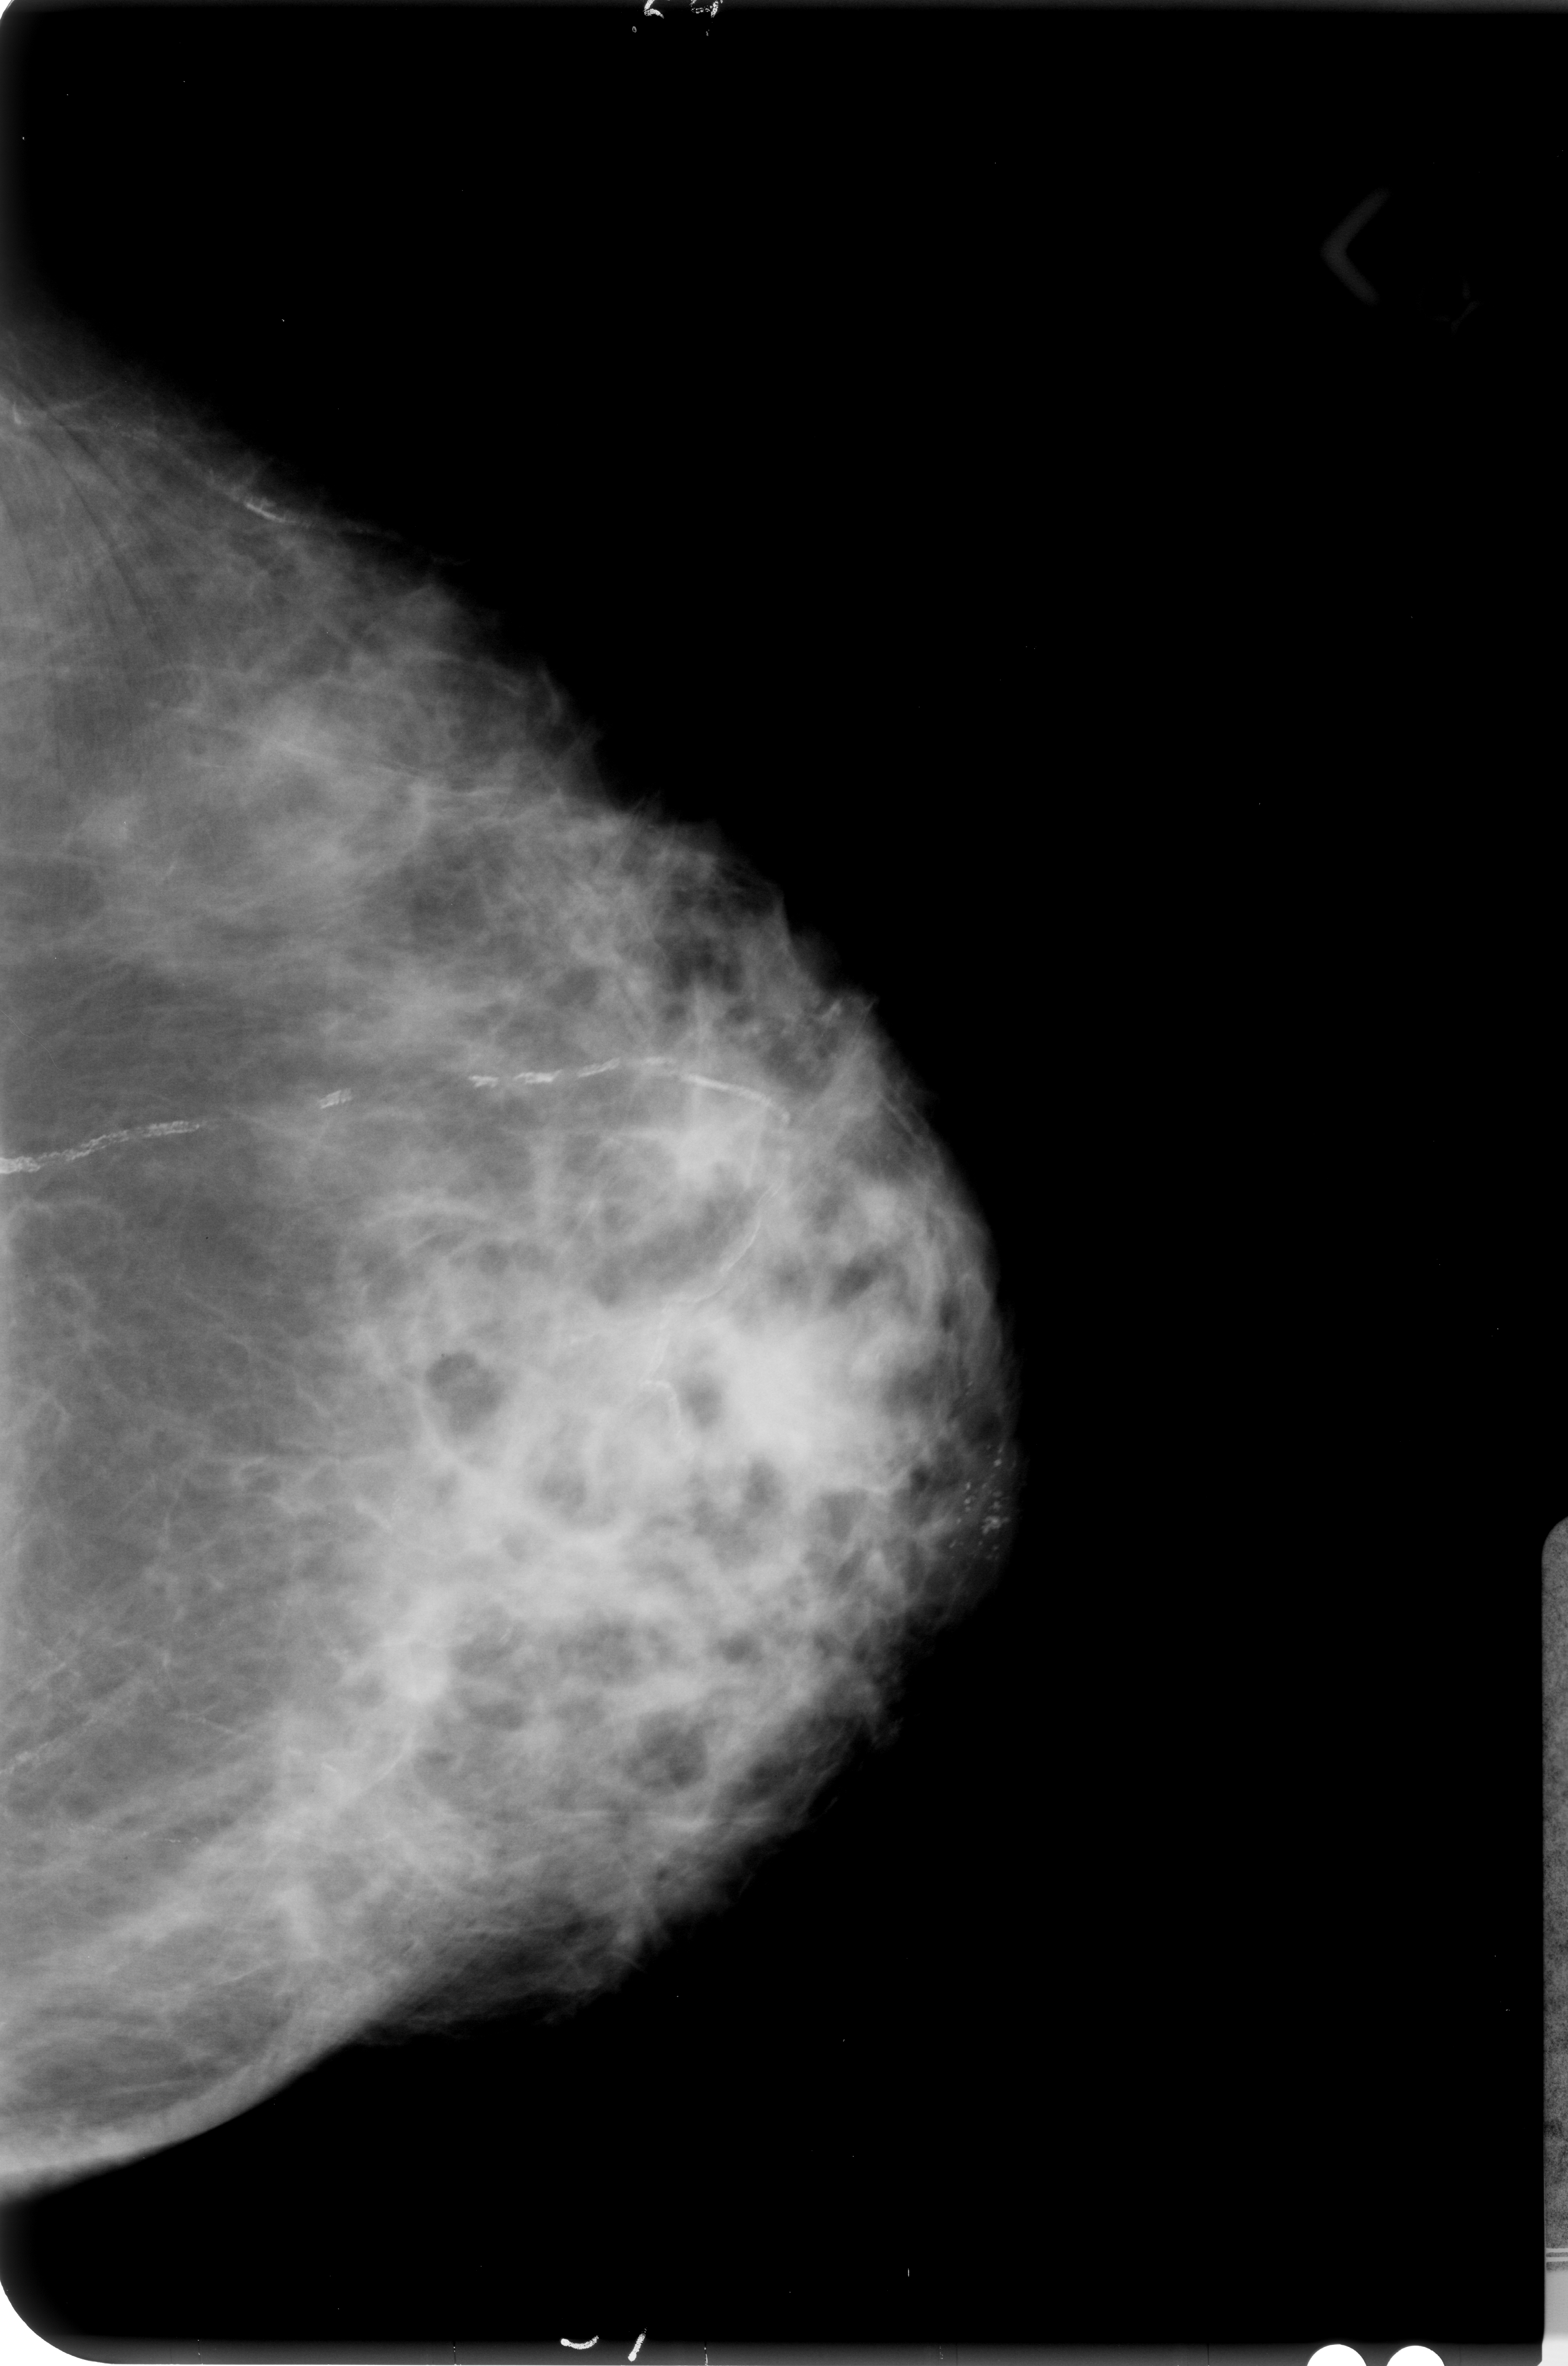
Digitized screen-film mammogram; left breast; craniocaudal (CC) view.
Marked findings (only marked abnormalities are described; nothing is implied about the rest of the image): calcifications, morphology pleomorphic, distribution clustered; BI-RADS assessment category 4; pathology result (as recorded, not read from the image): malignant.